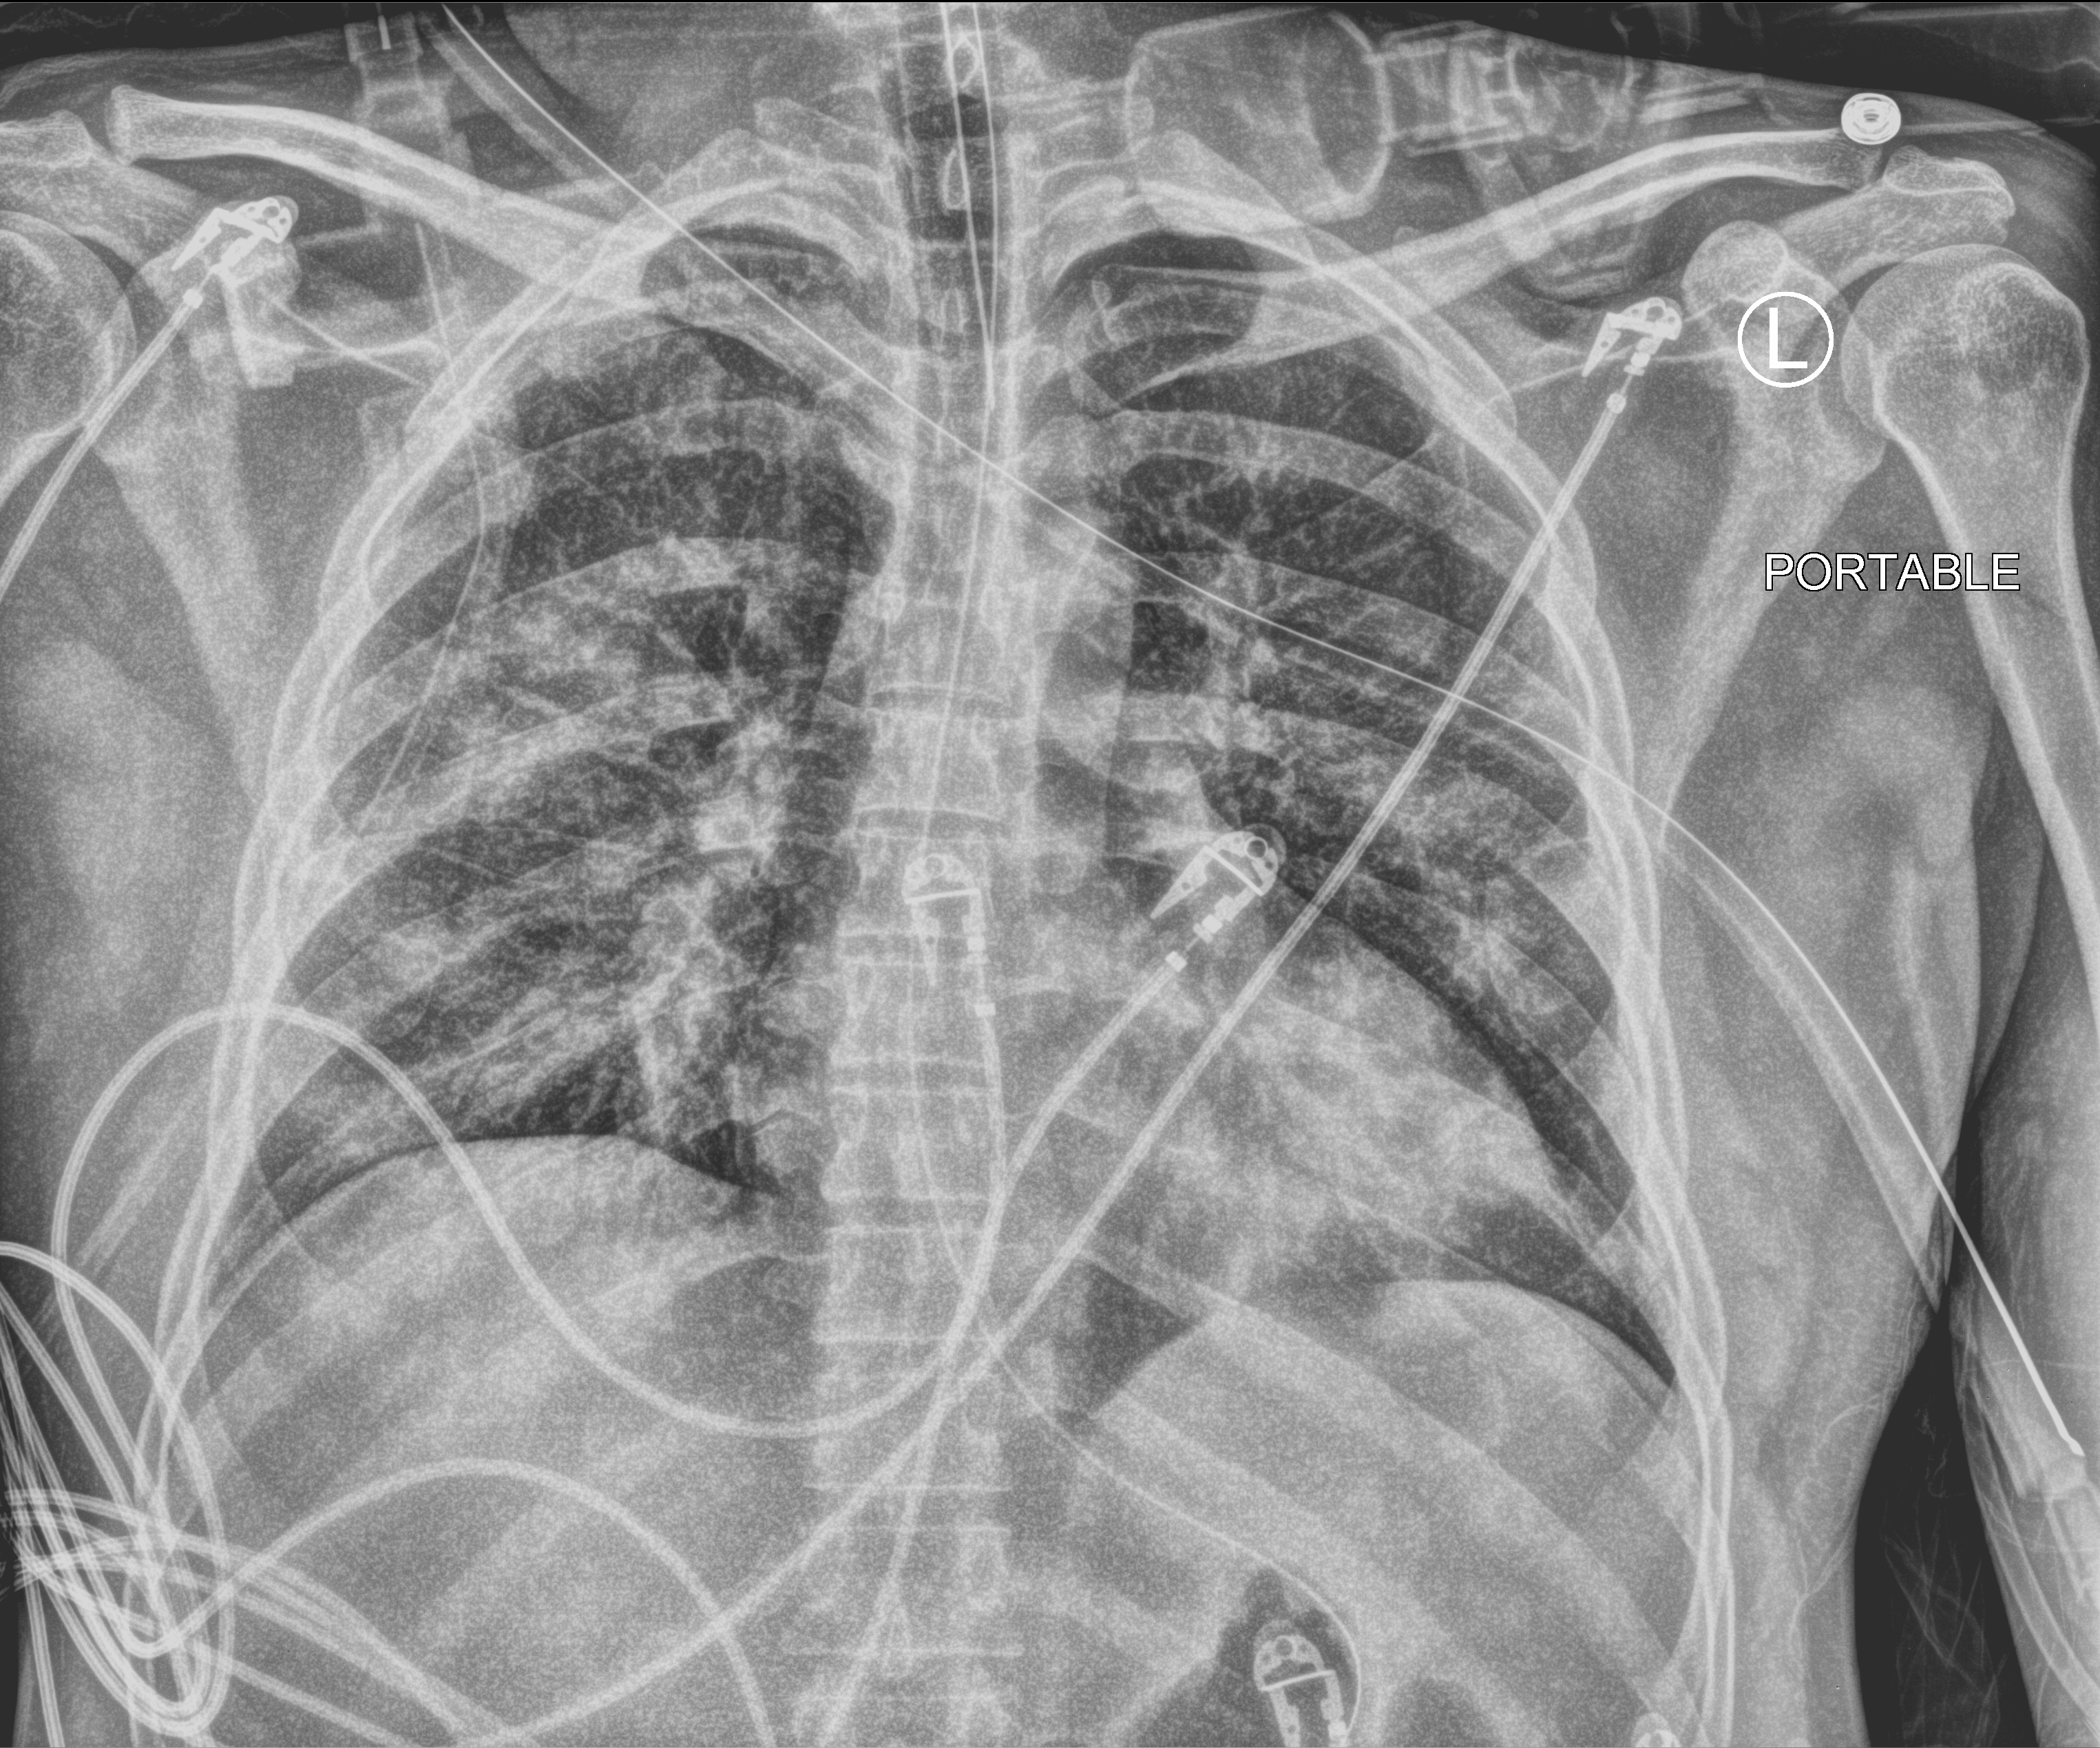
Bedside chest radiograph (computed radiography), anteroposterior (AP) projection. Patient hospitalised with COVID-19; male, aged 18–59 years.
Admission-level facts for this patient (not findings on this image; timing relative to this image not recorded): admitted to intensive care during this hospital stay: yes.